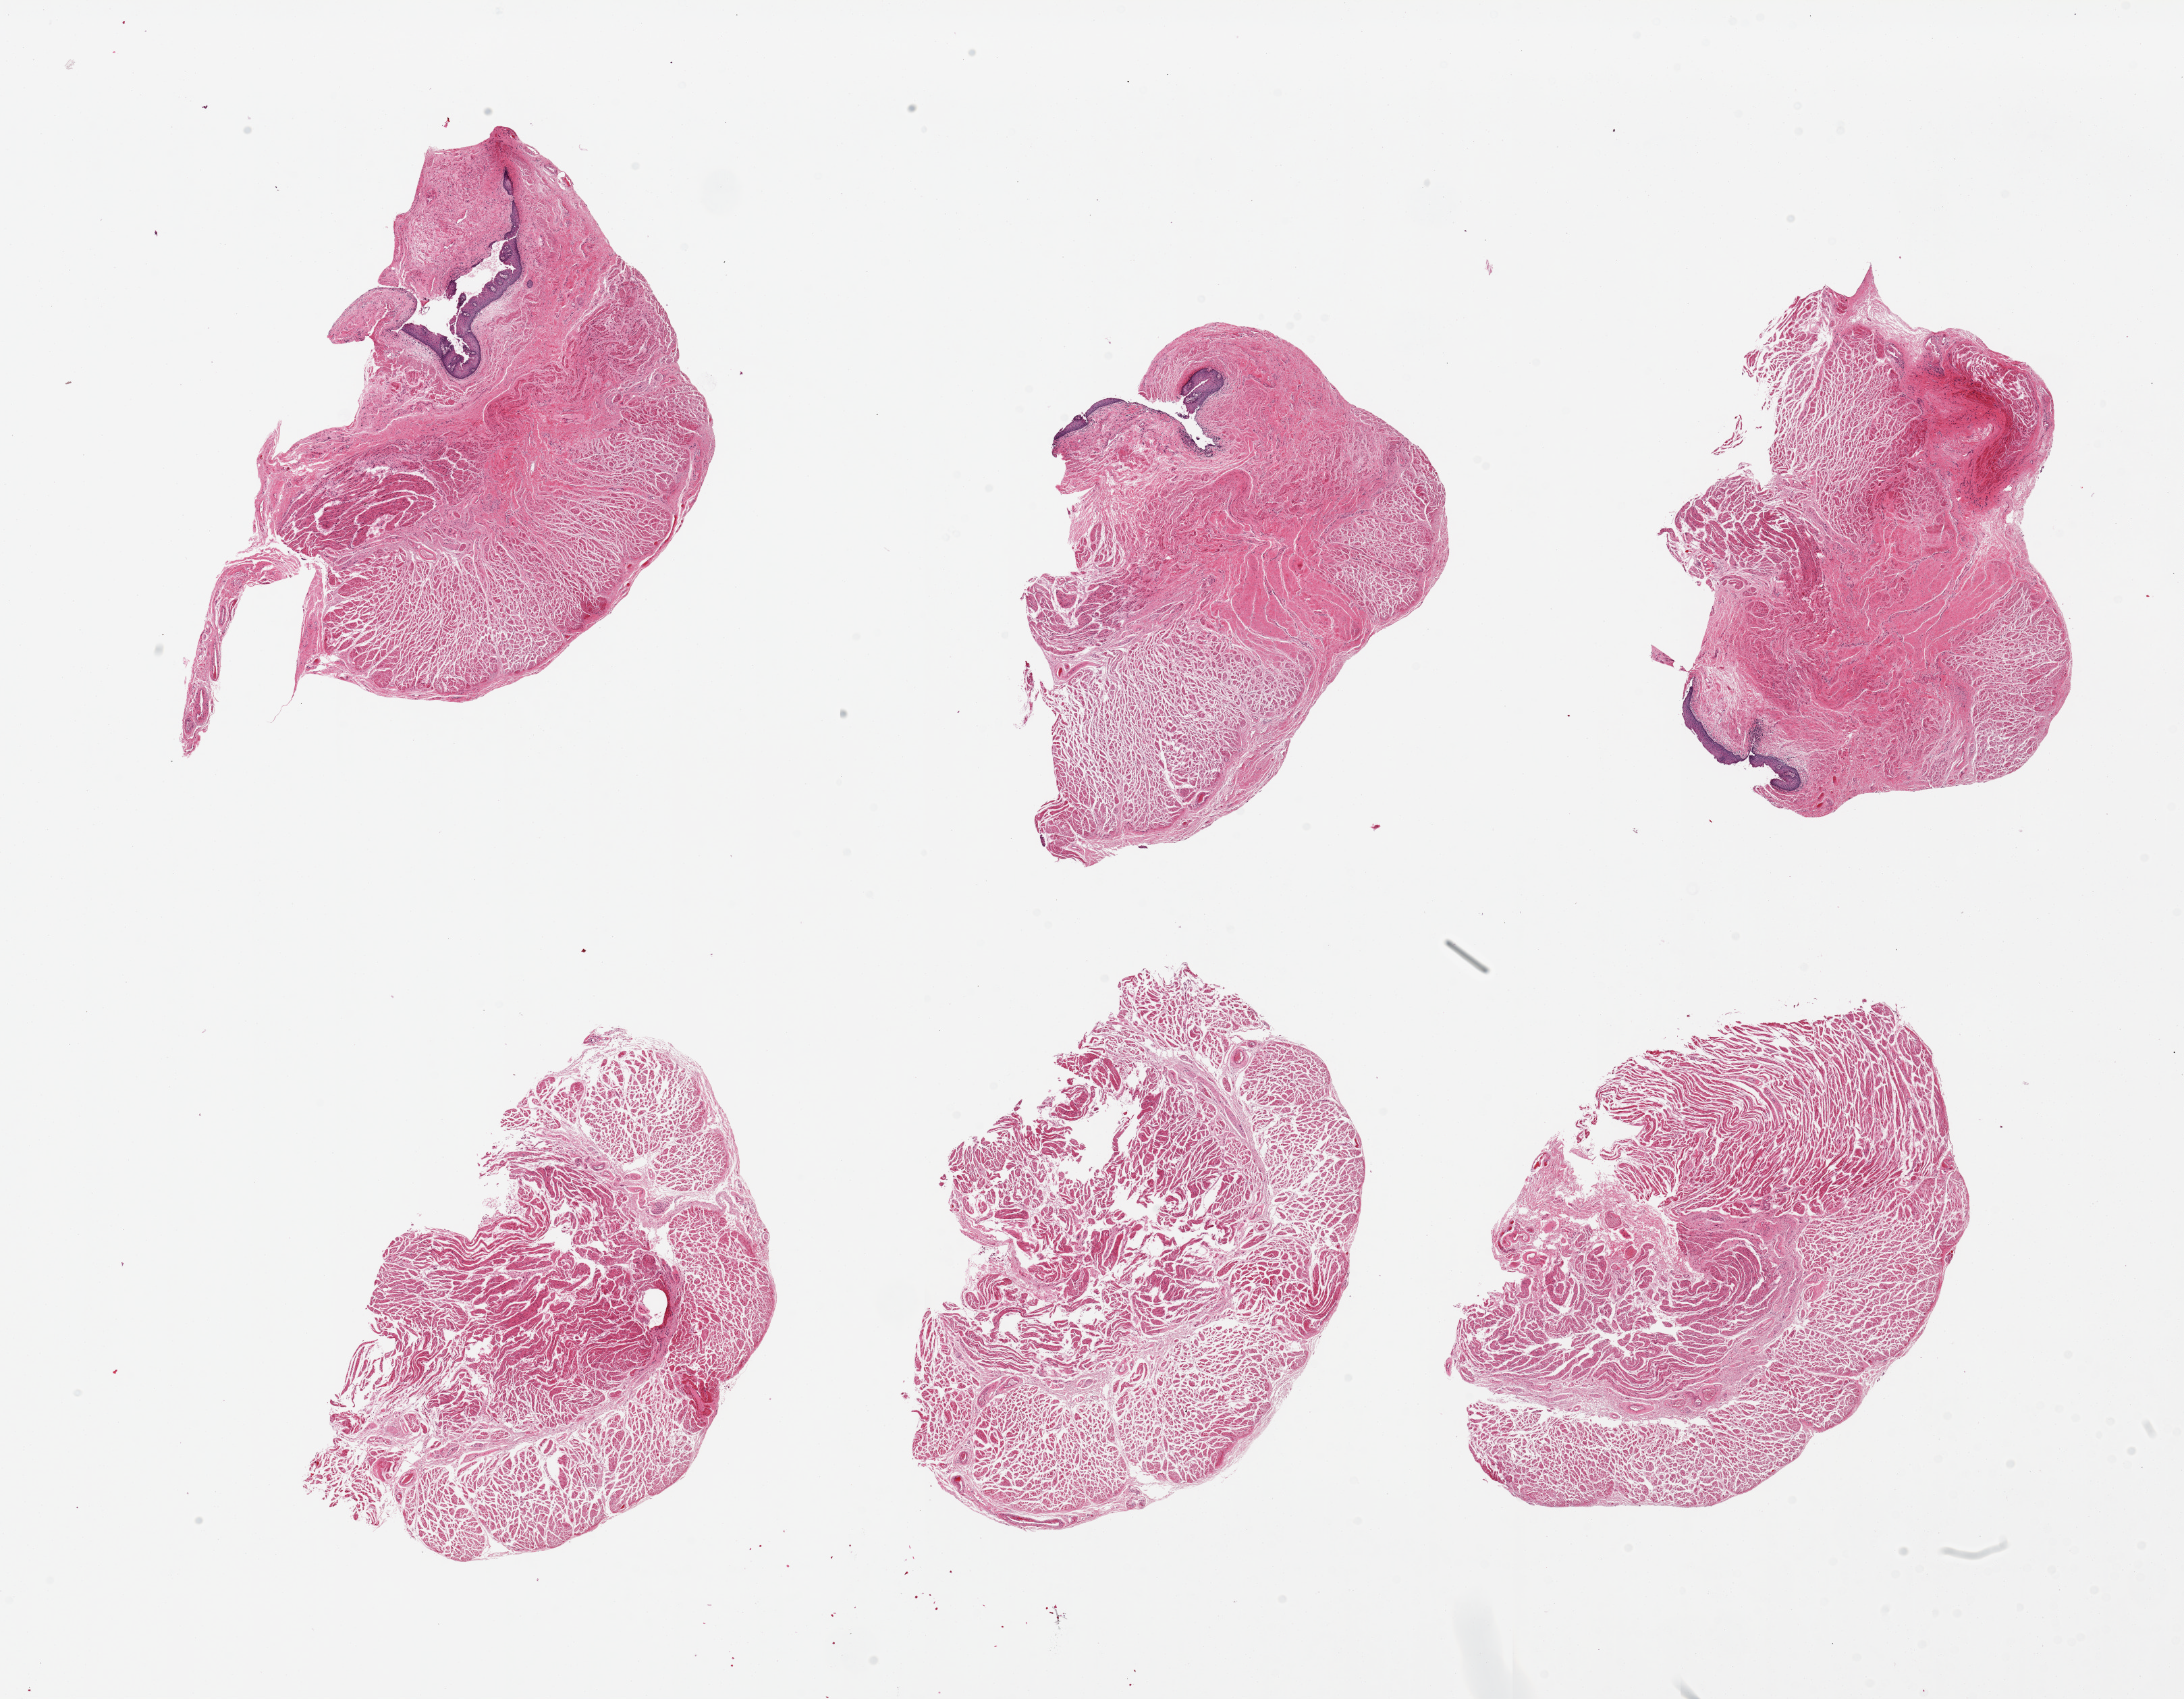
Whole-slide image, haematoxylin and eosin stain — a low-resolution overview of the entire scanned area, about 25.6 x 19.9 mm. PAXgene-fixed, paraffin-embedded tissue. Sampled site (target tissue): gastroesophageal junction. Donor tissue sample. Donor: male.
Reviewer comment on this tissue sample: 6 pieces, three with residual squamous mucosa.